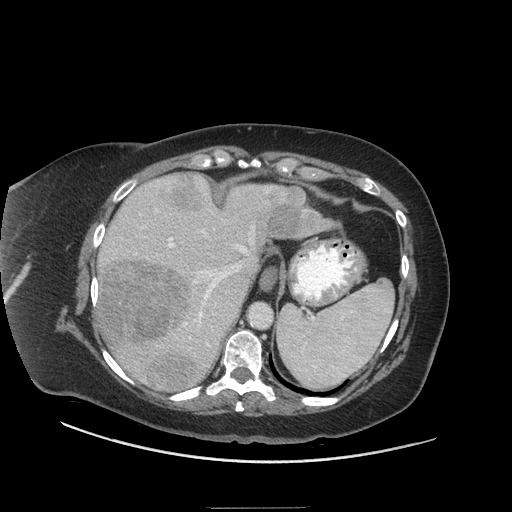
Contrast-enhanced abdominal CT (liver protocol), one axial slice; reconstruction kernel STANDARD; 140 kVp; soft-tissue window (W 400 / L 40 HU); 512 × 512 image matrix, field of view 440 × 440 mm. From the clinical record (not read from this slice): diagnosis: hepatocellular carcinoma (patient treated with transarterial chemoembolisation; whether this scan precedes or follows treatment is not stated here); TNM stage (as recorded): Stage-II; Child-Pugh class: A; tumour differentiation: moderately differentiated; tumour nodularity: multinodular.
Structures marked on this image (semi-automatically segmented with operator editing):
- liver parenchyma outside the tumour (the mass and vessels are separate outlines, so this box may not span the whole liver): box from (x=94, y=174) to (x=306, y=390) px
- mass: (x=97, y=174)–(x=336, y=393)
- liver vessels: (x=110, y=181)–(x=271, y=349)